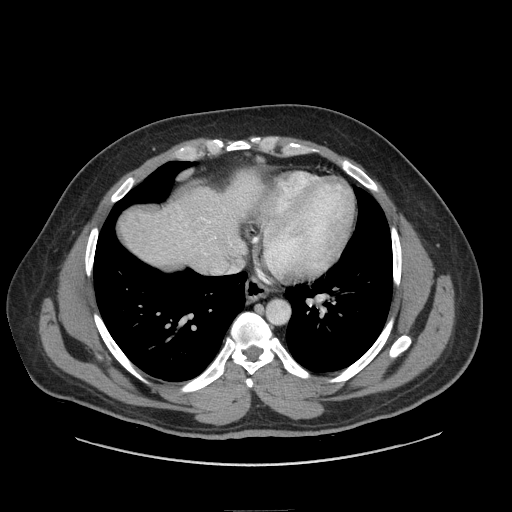
Contrast-enhanced abdominal CT (liver protocol), one axial slice. Slice 76 of 87 in the series (ordered by position). Reconstruction kernel STANDARD. 140 kVp. Soft-tissue window (W 400 / L 40 HU). 2.5 mm slice thickness. 512 × 512 image matrix, field of view 440 × 440 mm. Case-level facts recorded for this patient, not image findings: diagnosis: hepatocellular carcinoma (patient treated with transarterial chemoembolisation; whether this scan precedes or follows treatment is not stated here); TNM stage (as recorded): Stage-II; Child-Pugh class: A.
Annotated regions visible in this slice (semi-automatically segmented with operator editing):
- abdominal aorta: bounding box [x1, y1, x2, y2] px = [267, 301, 289, 324]
- liver parenchyma outside the tumour (the mass and vessels are separate outlines, so this box may not span the whole liver): [118, 176, 260, 270]